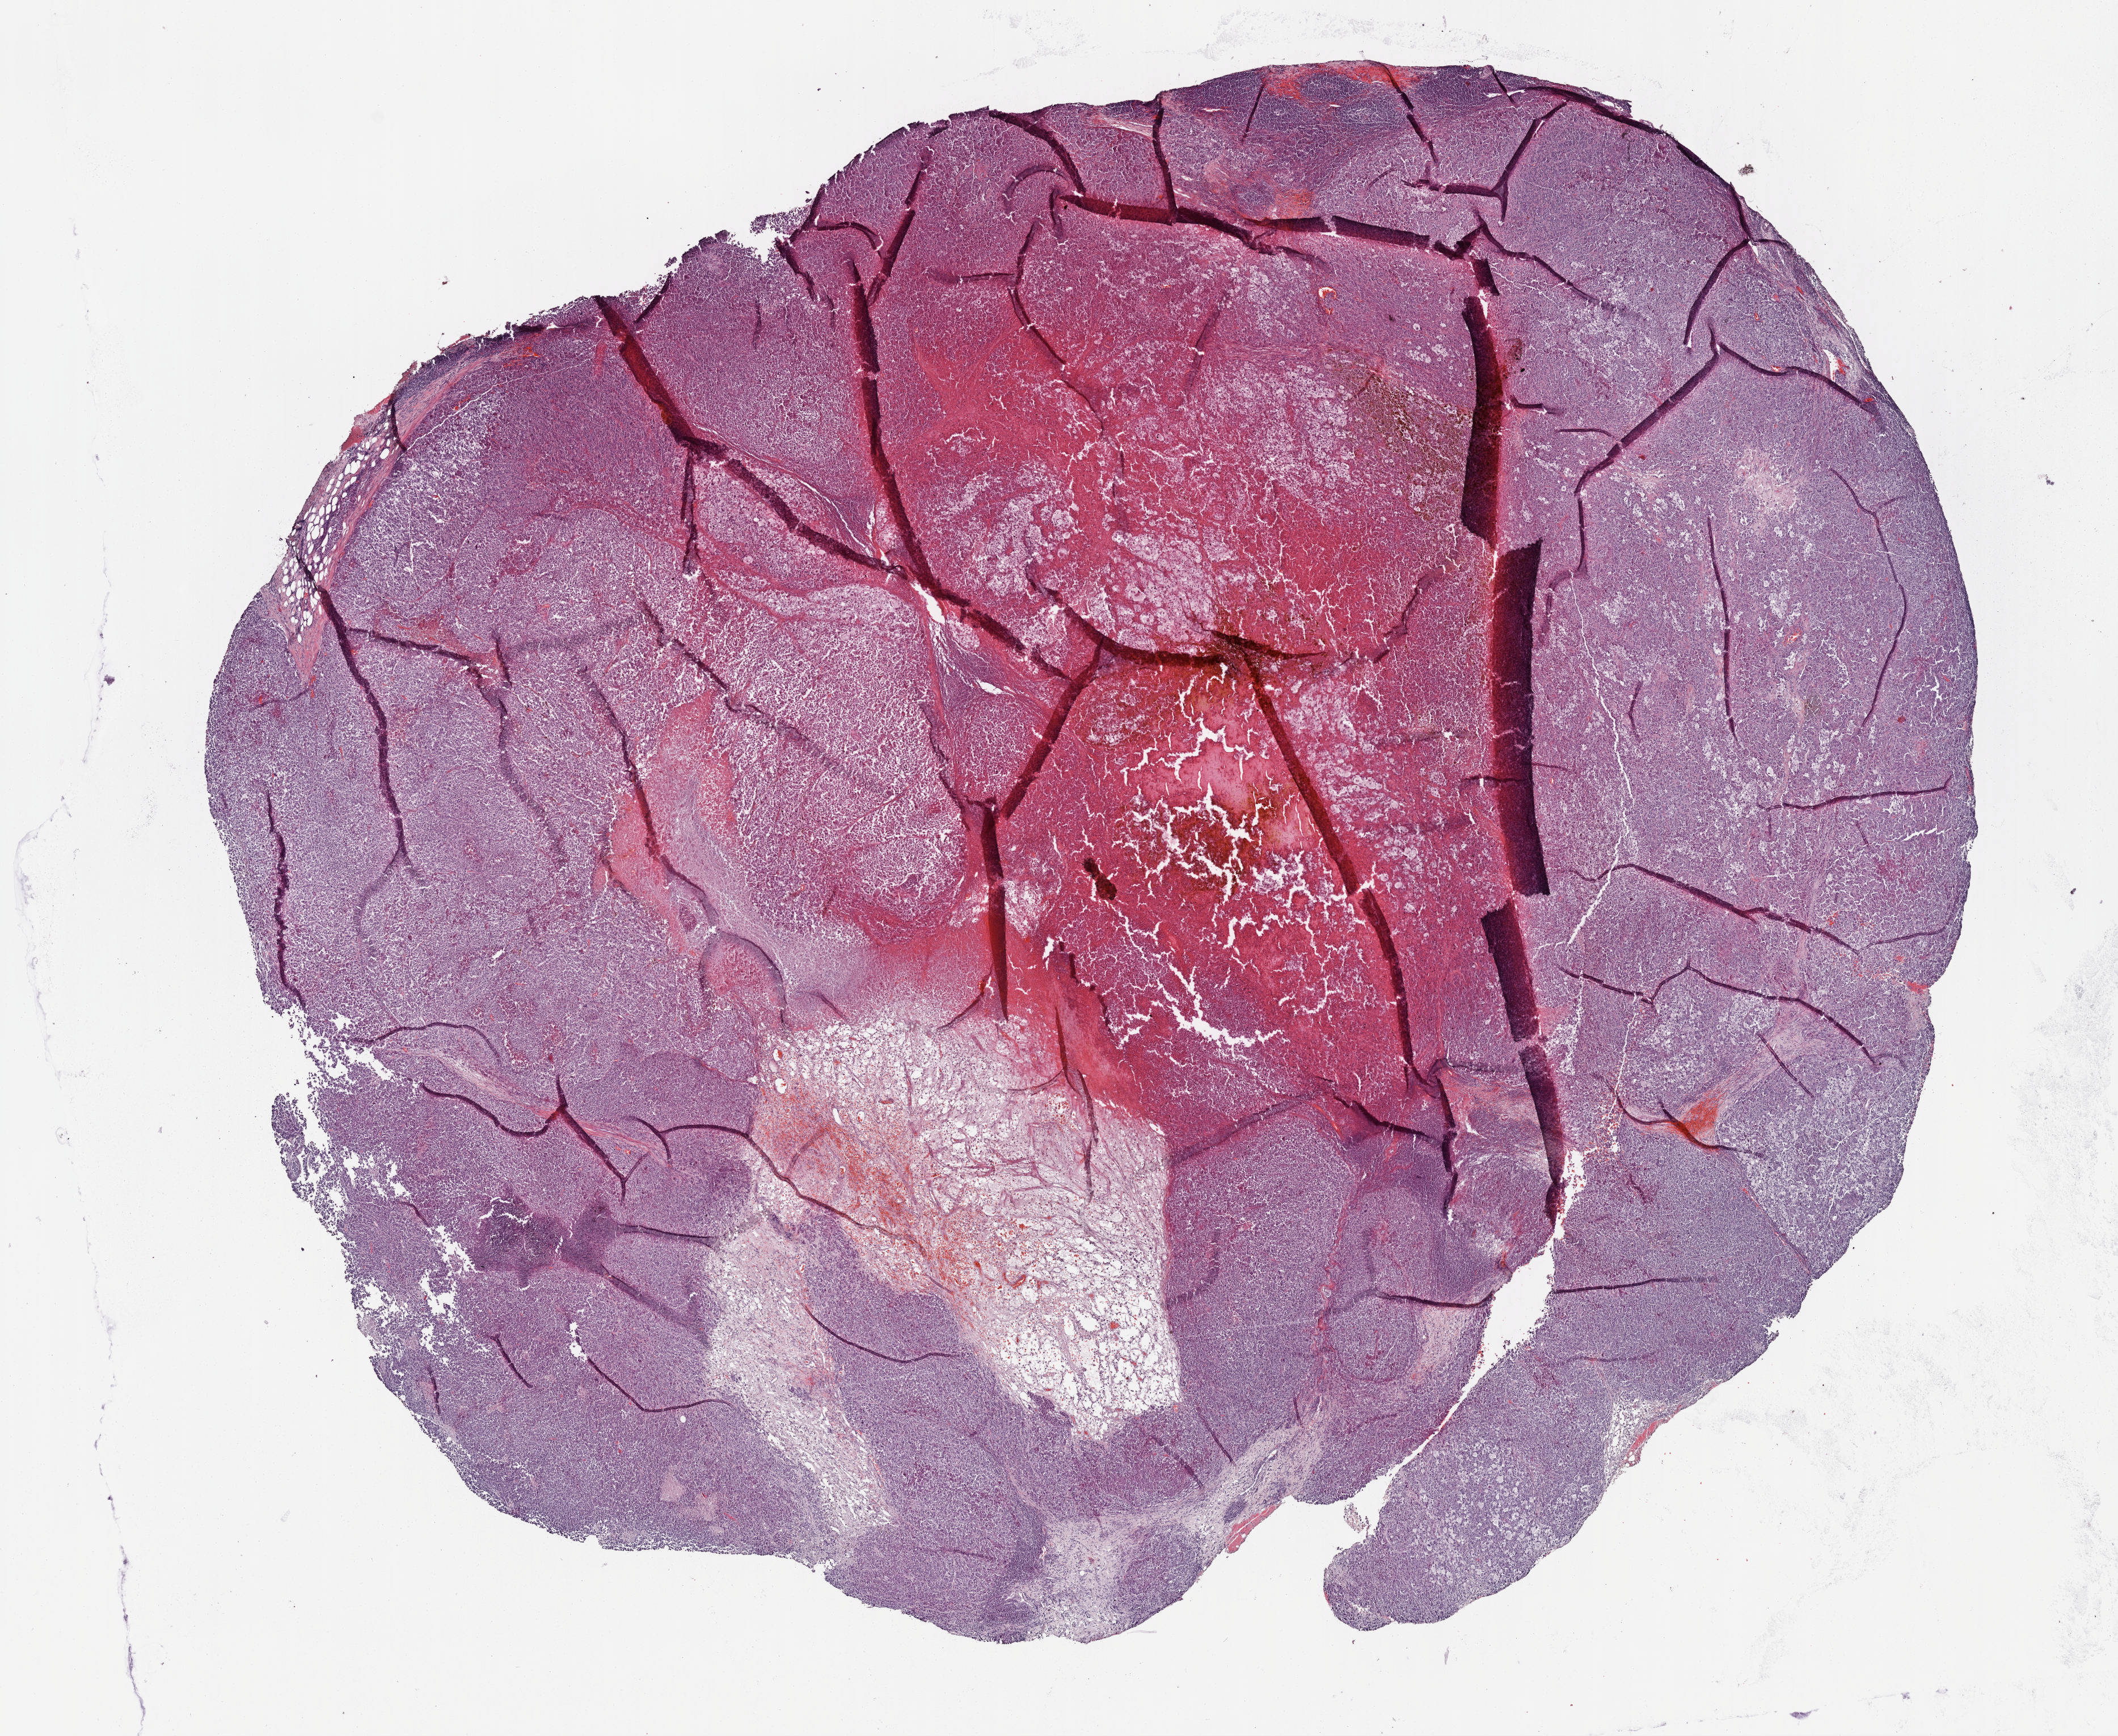
H&E-stained whole-slide image, shown as a low-resolution overview of the whole scanned area (about 15.1 x 12.4 mm, slide scanned at 40x), FFPE section, sample: primary tumour, skin. Male, age 85 years at initial diagnosis.
* histologic diagnosis: Malignant melanoma, NOS